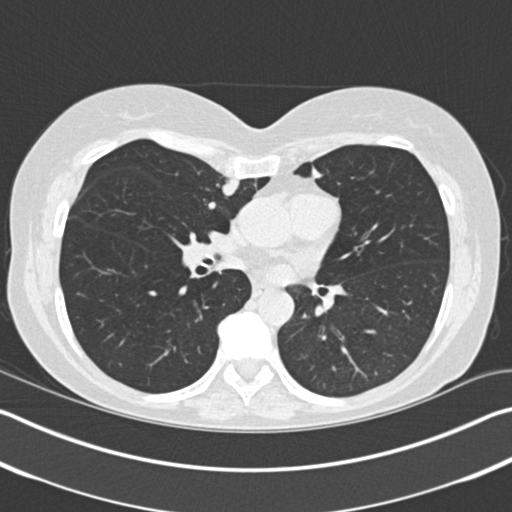
Low-dose screening chest CT, one axial slice. Slice 95 of 183 in the series (ordered by position). Reconstruction kernel B30f. Lung window (W 1500 / L -600 HU). 2 mm slice thickness. 512 × 512 image matrix, field of view 340 × 340 mm.
Structures marked on this image (outlined manually by an expert reader):
- lesion 1 (tumor, upper lobe of right lung): bounding box (x1, y1, x2, y2) in pixels: (222, 178, 240, 196)